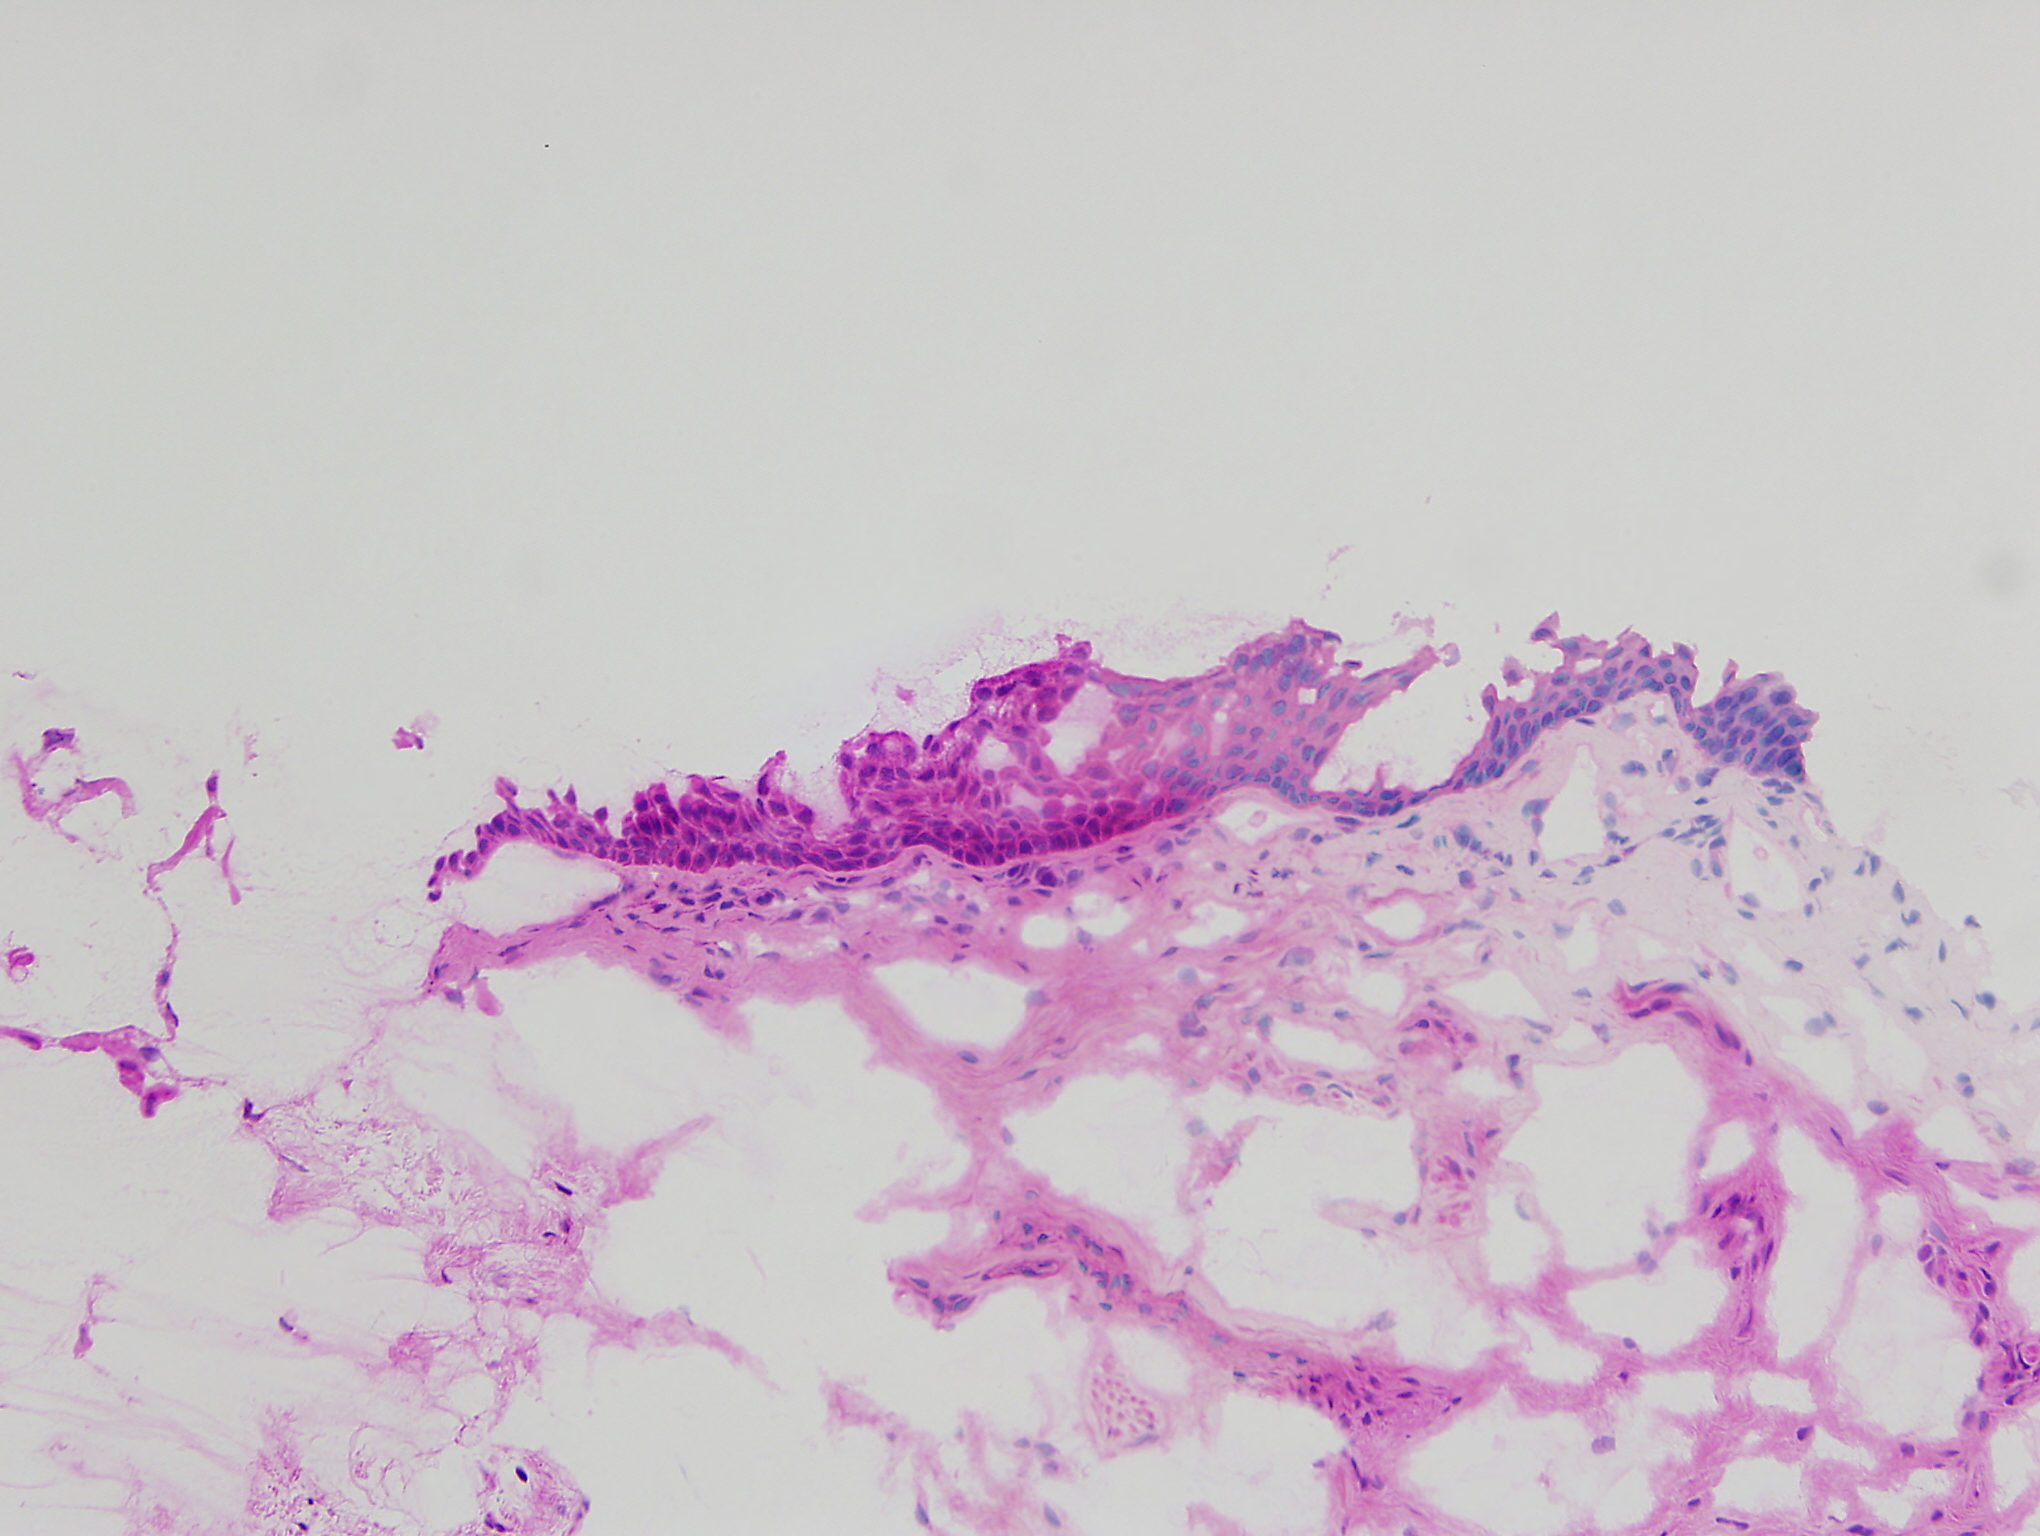
Hematoxylin and eosin (H&E) stained micrograph of a single small tissue field — about 1.0 x 0.8 mm across. Frozen section. Sample: solid tissue normal (non-tumour tissue), head and neck. Patient: male, age at initial diagnosis 62 years.
This section: solid tissue normal sample (biorepository sample class). Patient diagnosis: Squamous cell carcinoma, NOS (larynx, NOS).